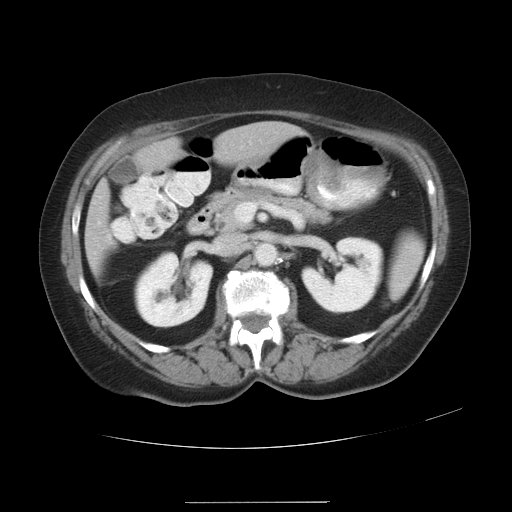
Contrast-enhanced abdominal CT, one axial slice. Slice 14 of 32 in the series (ordered by position). Reconstruction kernel STANDARD. 120 kVp. Soft-tissue window (W 400 / L 40 HU). 7.5 mm slice thickness. 512 × 512 image matrix, field of view 386 × 386 mm. Female patient, age 65 years. From the clinical record (not read from this slice): diagnosis: colorectal cancer liver metastases, imaged before liver resection; multiple liver metastases: yes; largest metastasis: 1.7 cm; disease in both lobes: no.
Structures marked on this image (outlined manually by an expert reader):
- liver: bounding box [x1, y1, x2, y2] px = [87, 124, 289, 262]
- planned liver remnant (the part of the liver to remain after resection): [87, 145, 175, 262]